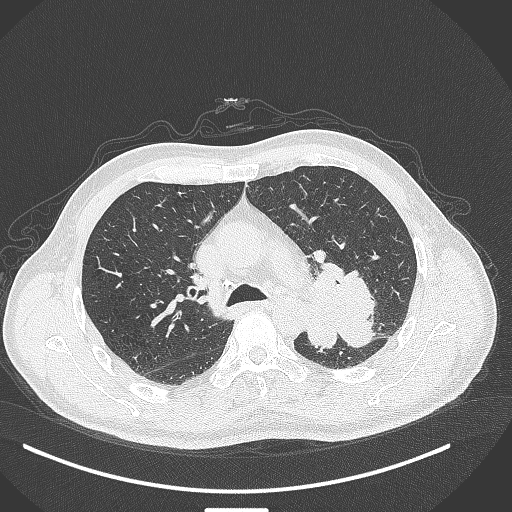
Chest CT, one axial slice; reconstruction kernel B70f; 120 kVp; lung window (W 1500 / L -600 HU); 1 mm slice thickness; 512 × 512 image matrix, field of view 400 × 400 mm. Male patient, age 55 years. From the clinical record (not read from this slice): clinical TNM (as recorded): T3 N0 M1c; histopathological grade: G3.
Structures marked on this image (bounding box drawn by a radiologist):
- lung tumour (recorded histology: adenocarcinoma): bounding box [x1, y1, x2, y2] px = [301, 257, 387, 369]